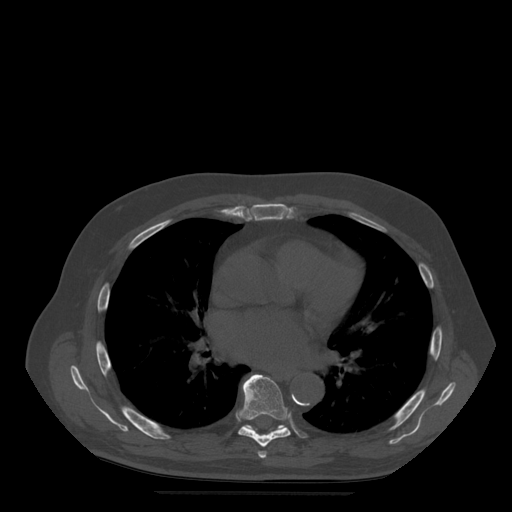
CT including the spine, one axial slice; slice 330 of 522 in the series (ordered by position); bone window (W 1800 / L 400 HU); 512 × 512 image matrix, field of view 420 × 420 mm. Patient age 72 years. Case-level facts recorded for this patient, not image findings: primary cancer: prostate.
Structures marked on this image (semi-automatic segmentation, software-assisted and operator-edited):
- T6 vertebra: bounding box (x1, y1, x2, y2) in pixels: (258, 451, 267, 459)
- T7 vertebra: (237, 375, 291, 448)
- T8 vertebra: (244, 425, 287, 432)